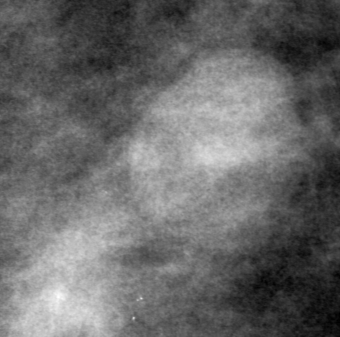
Crop from a digitized film mammogram around one marked abnormality; right breast; MLO view.
Finding: mass, shape oval, margins circumscribed; BI-RADS assessment category 0 (incomplete: needs additional imaging); subtlety rating 5 on a 1 (subtle) to 5 (obvious) scale; pathology result (as recorded, not read from the image): benign.